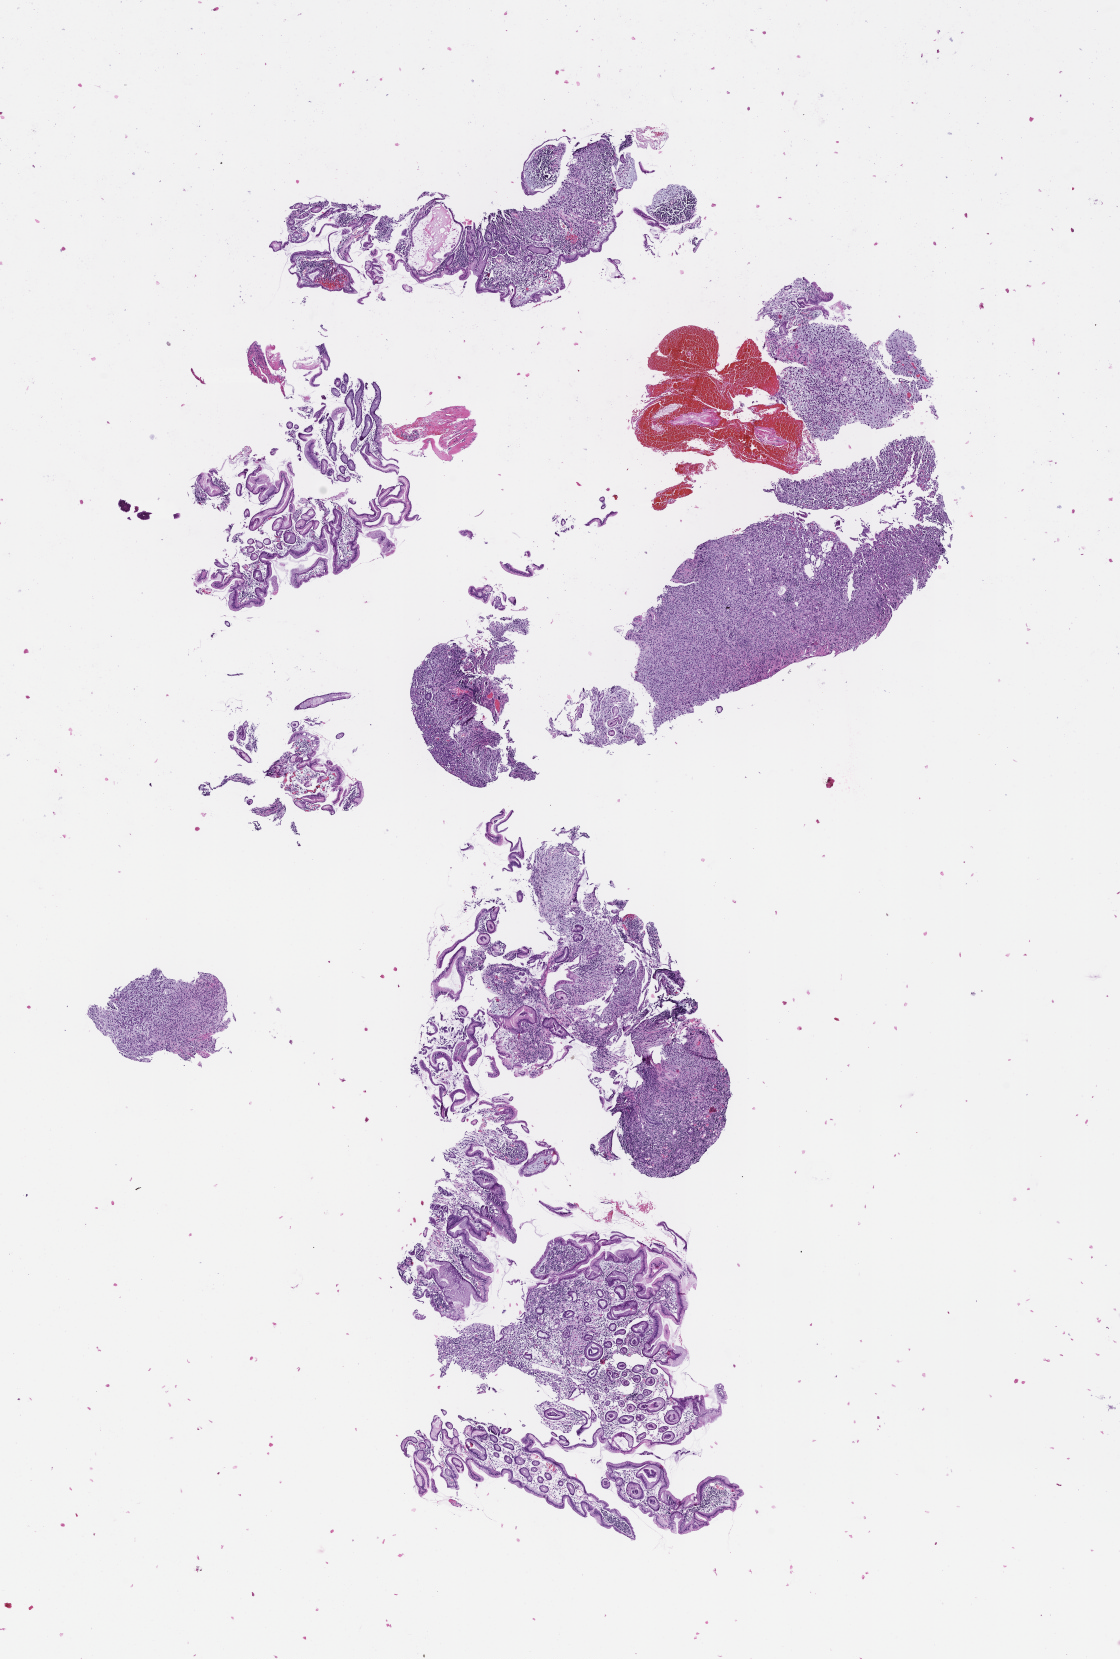
Haematoxylin and eosin whole-slide image, low-resolution overview of the scanned area, about 9.0 x 13.4 mm; formalin-fixed, paraffin-embedded (FFPE) tissue; tissue site: stomach; specimen time point: archival tissue. Patient sex: female.
This section: primary tumor. Diagnosis: Adenocarcinoma of the Gastroesophageal Junction.